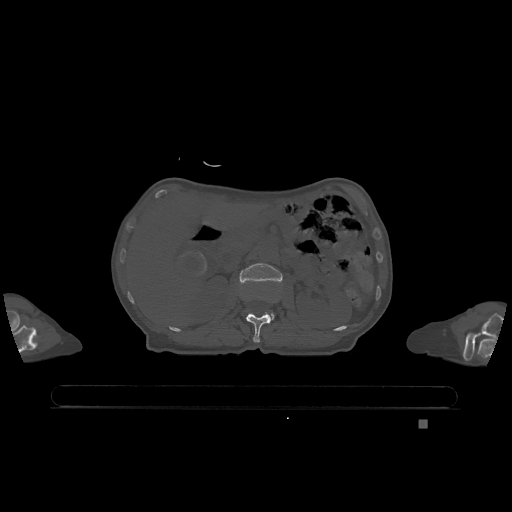
CT including the spine, one axial slice; position 454 of 1317 along the scan axis; bone window (W 1800 / L 400 HU); 512 × 512 image matrix. Female patient, age 74 years. From the clinical record (not read from this slice): primary cancer: lung; vertebrae with lytic lesions (as recorded): T1, T4, T5, T6, L4, L5.
Annotated regions visible in this slice (semi-automatic segmentation, software-assisted and operator-edited):
- L1 vertebra: bounding box [x1, y1, x2, y2] px = [246, 313, 271, 343]
- L2 vertebra: [239, 263, 283, 320]